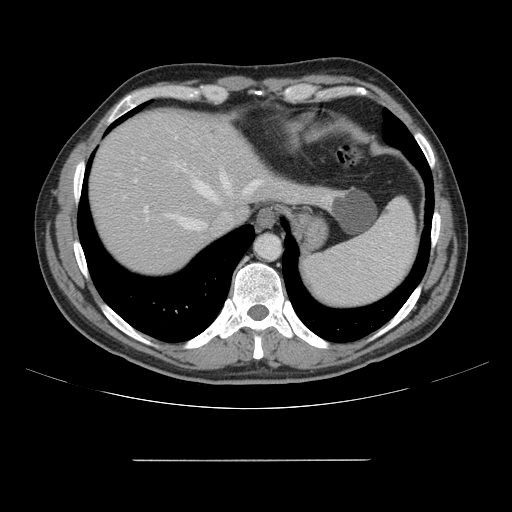
Contrast-enhanced abdominal CT, one axial slice; position 130 of 164 along the scan axis; intravenous contrast given; soft-tissue window (W 400 / L 40 HU); 2.5 mm slice thickness; 512 × 512 image matrix, field of view 404 × 404 mm. Male patient, age 54 years. Case-level facts recorded for this patient, not image findings: diagnosis: colorectal cancer liver metastases, imaged before liver resection; multiple liver metastases: yes; largest metastasis: 1 cm; disease in both lobes: no.
Outlined on this slice (outlined manually by an expert reader):
- hepatic veins: bounding box <166,175,262,230> (left, top, right, bottom; pixels)
- liver: <91,111,326,274>
- planned liver remnant (the part of the liver to remain after resection): <91,111,253,274>
- portal vein (with intrahepatic branches): <134,137,230,221>